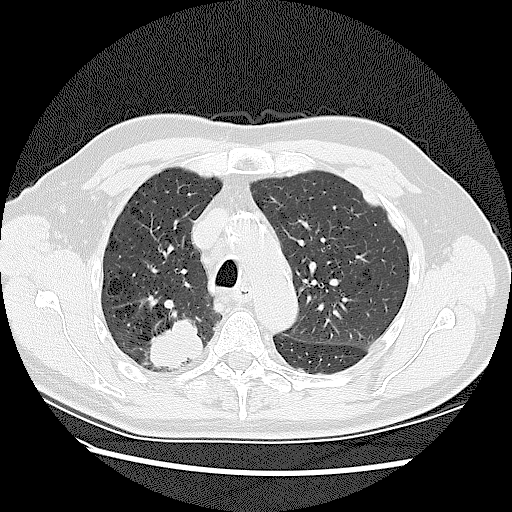
Chest CT (low-dose screening protocol), one axial image, baseline annual screen, lung window (W 1500 / L -600 HU), 2.5 mm slice thickness, lung (sharp) reconstruction kernel (LUNG). Male, age 72 years at enrolment. Current smoker at enrolment.
Expert-annotated lung lesion, bounding box <139,311,213,376> (left, top, right, bottom; pixels). The screening reader recorded 2 non-calcified nodules or masses ≥4 mm on this exam; which of them this box marks is not recorded. Later outcome: lung cancer diagnosed 42 days after this screen — adenocarcinoma, NOS, right upper lobe, stage IV (AJCC 6th edition), 45 mm at pathology.